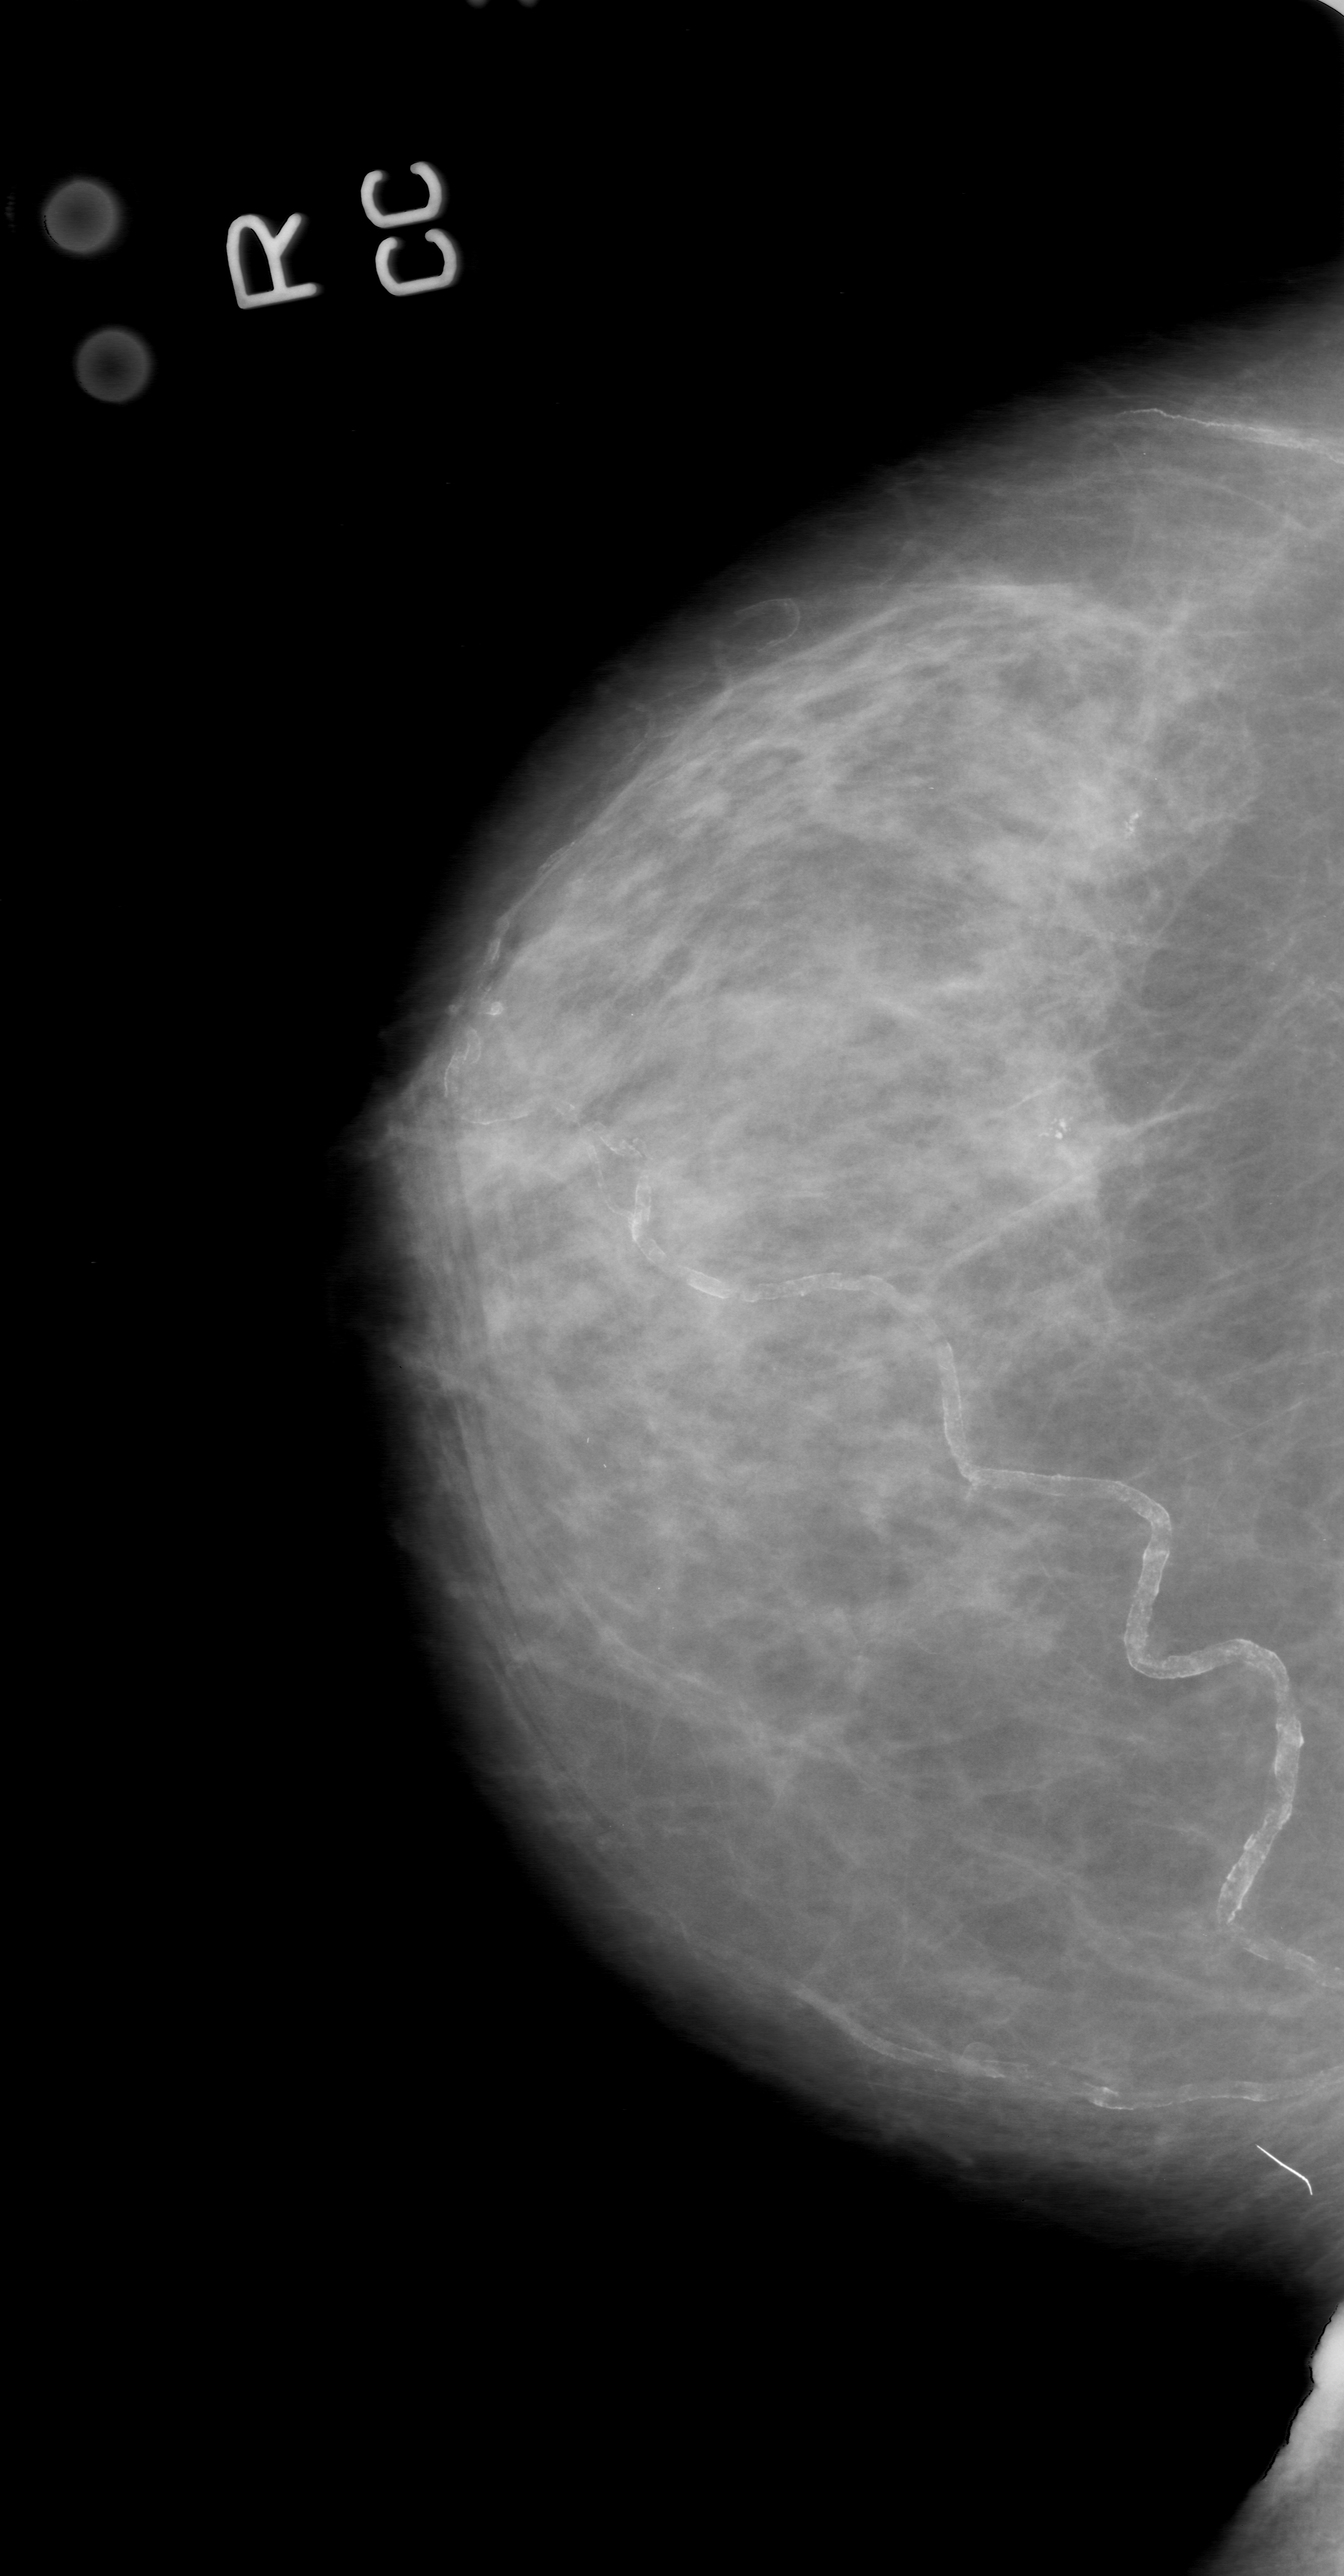
Digitized screen-film mammogram, right breast, CC view, breast composition: heterogeneously dense (BI-RADS density category 3 of 4).
Radiologist-marked abnormalities on this image: calcifications, morphology coarse, distribution clustered; BI-RADS assessment category 0 (incomplete: needs additional imaging); subtlety rating 5 on a 1 (subtle) to 5 (obvious) scale; pathology (as recorded): benign.